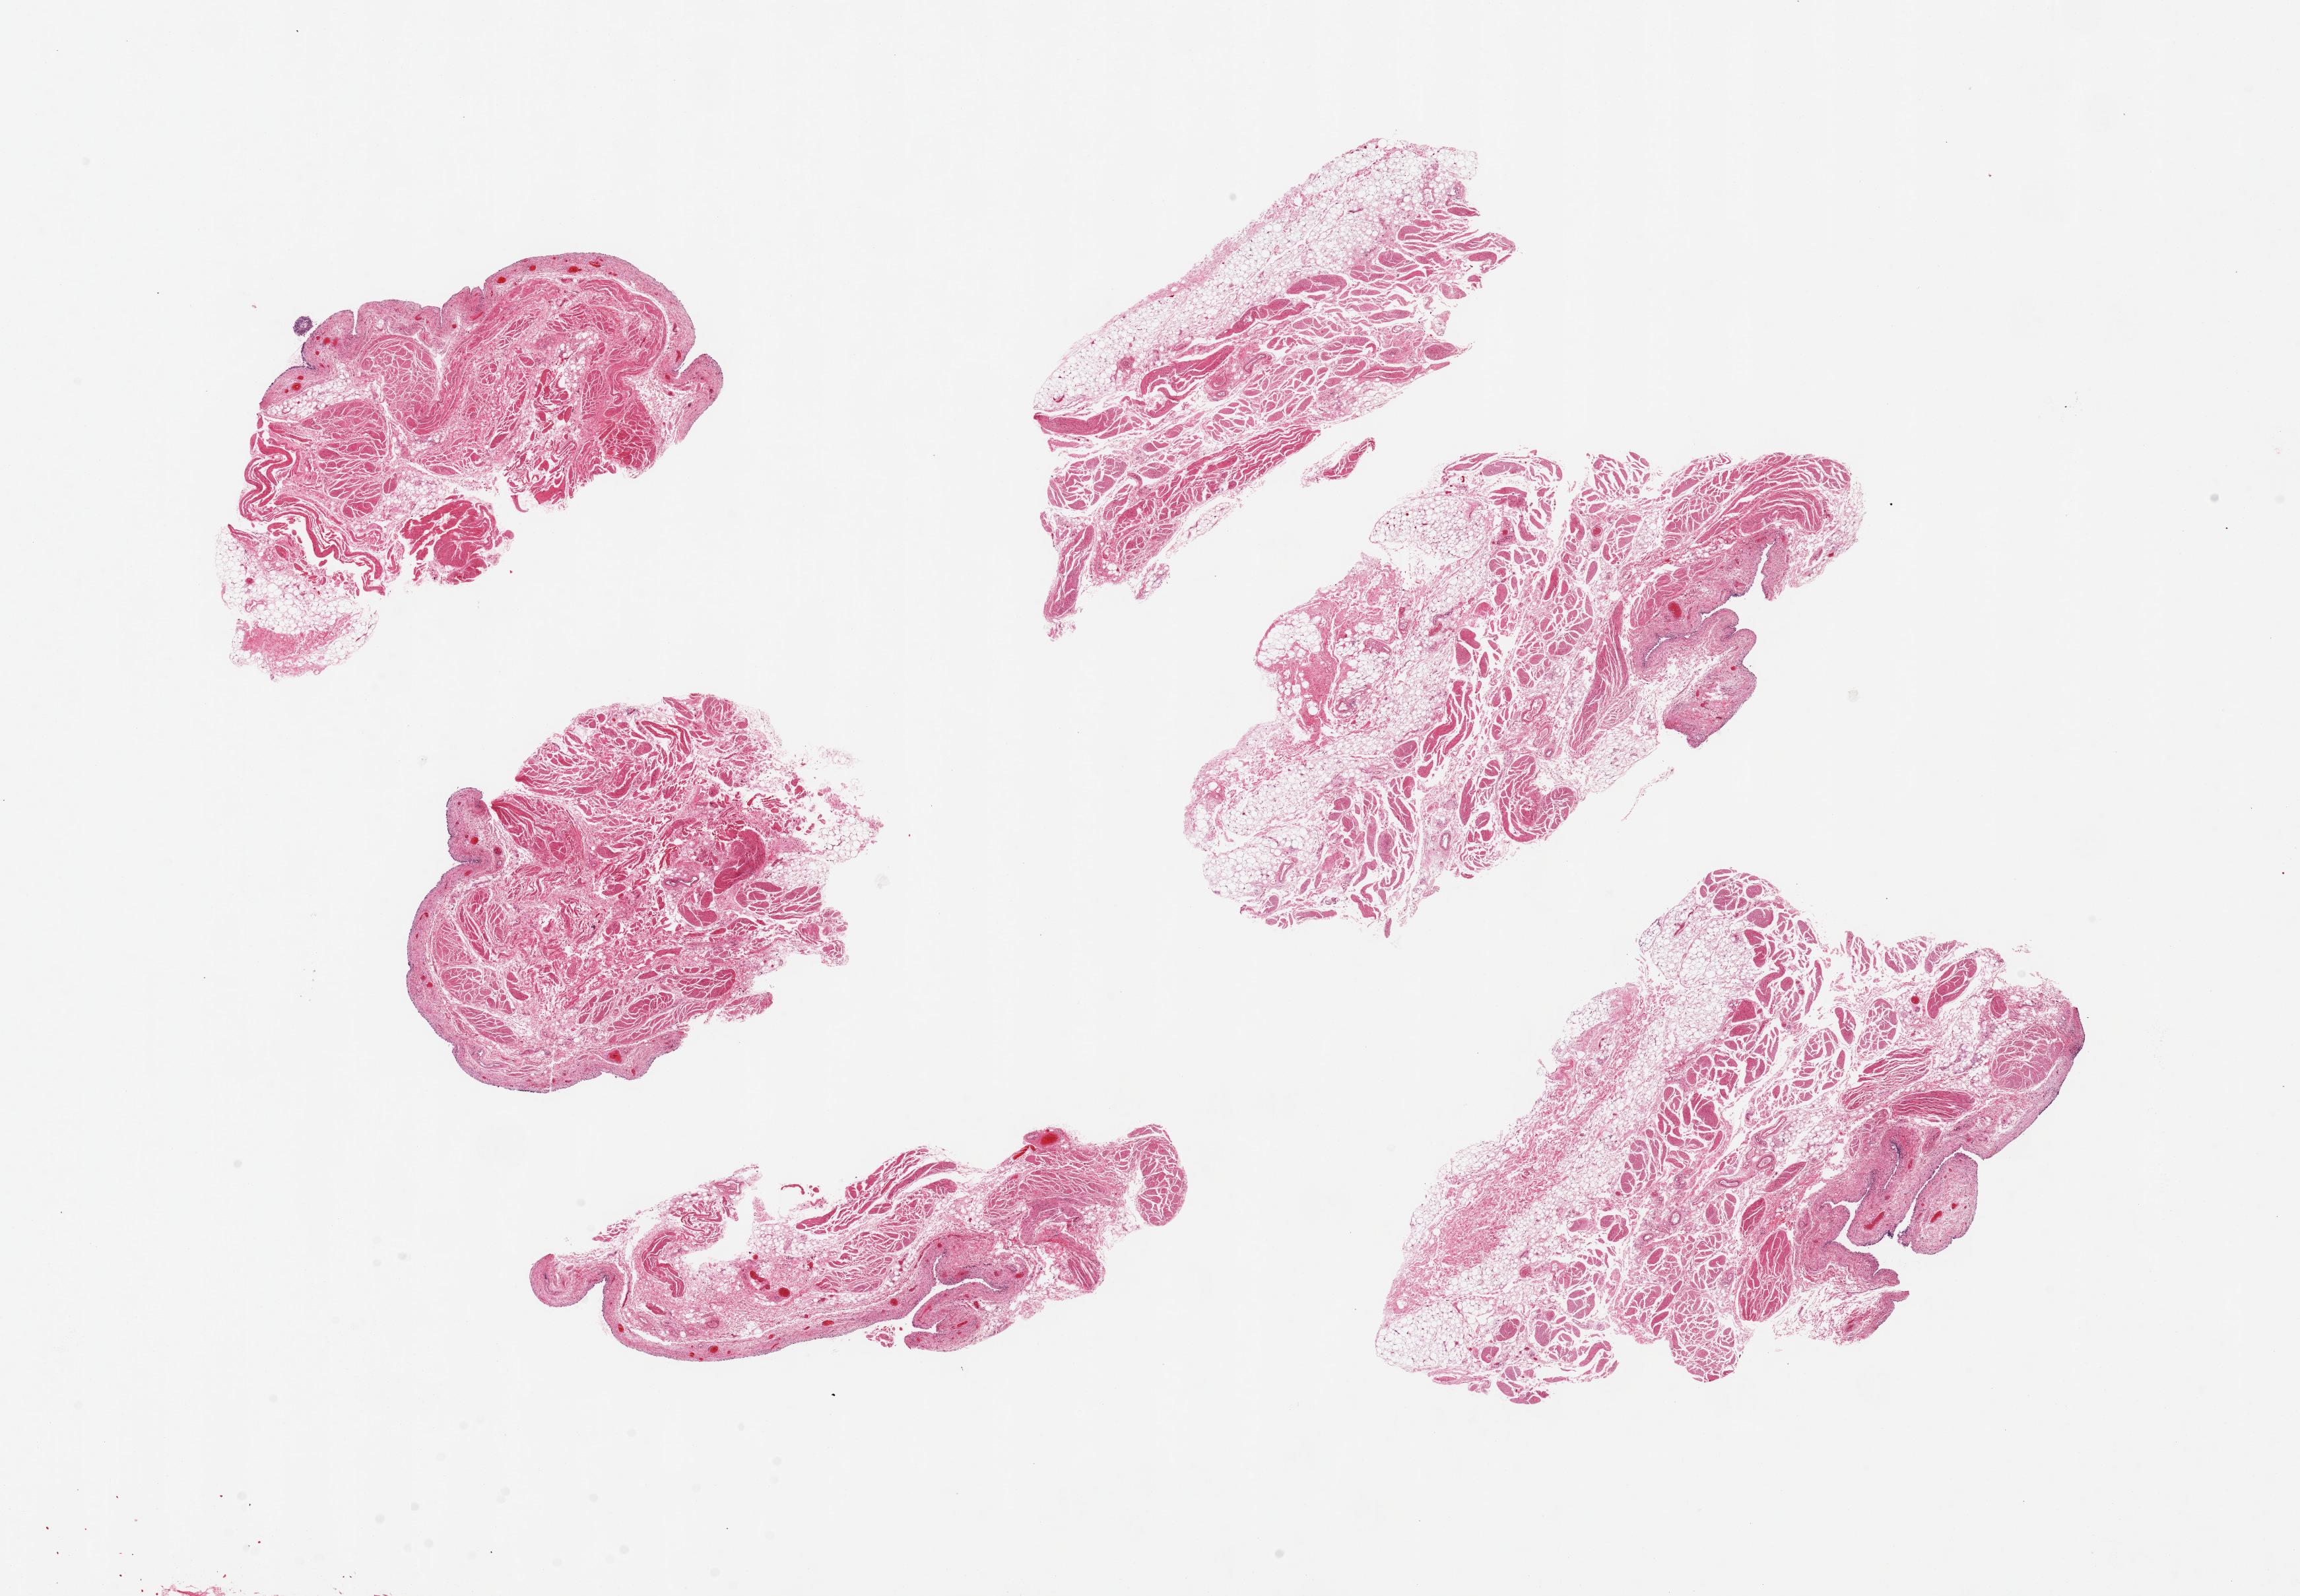
Whole-slide image, hematoxylin and eosin (H&E) stain, brightfield — shown as a low-resolution overview of the whole scanned area (about 27.6 x 19.1 mm, from a 20x scan). PAXgene-fixed paraffin-embedded (PFPE) section. Target tissue: urinary bladder. Donor tissue sample. Donor sex: female.
* pathologist's review note for this sample: 6 pieces, ~8x4mm. Urothelium completely sloughed, detrusor muscle only